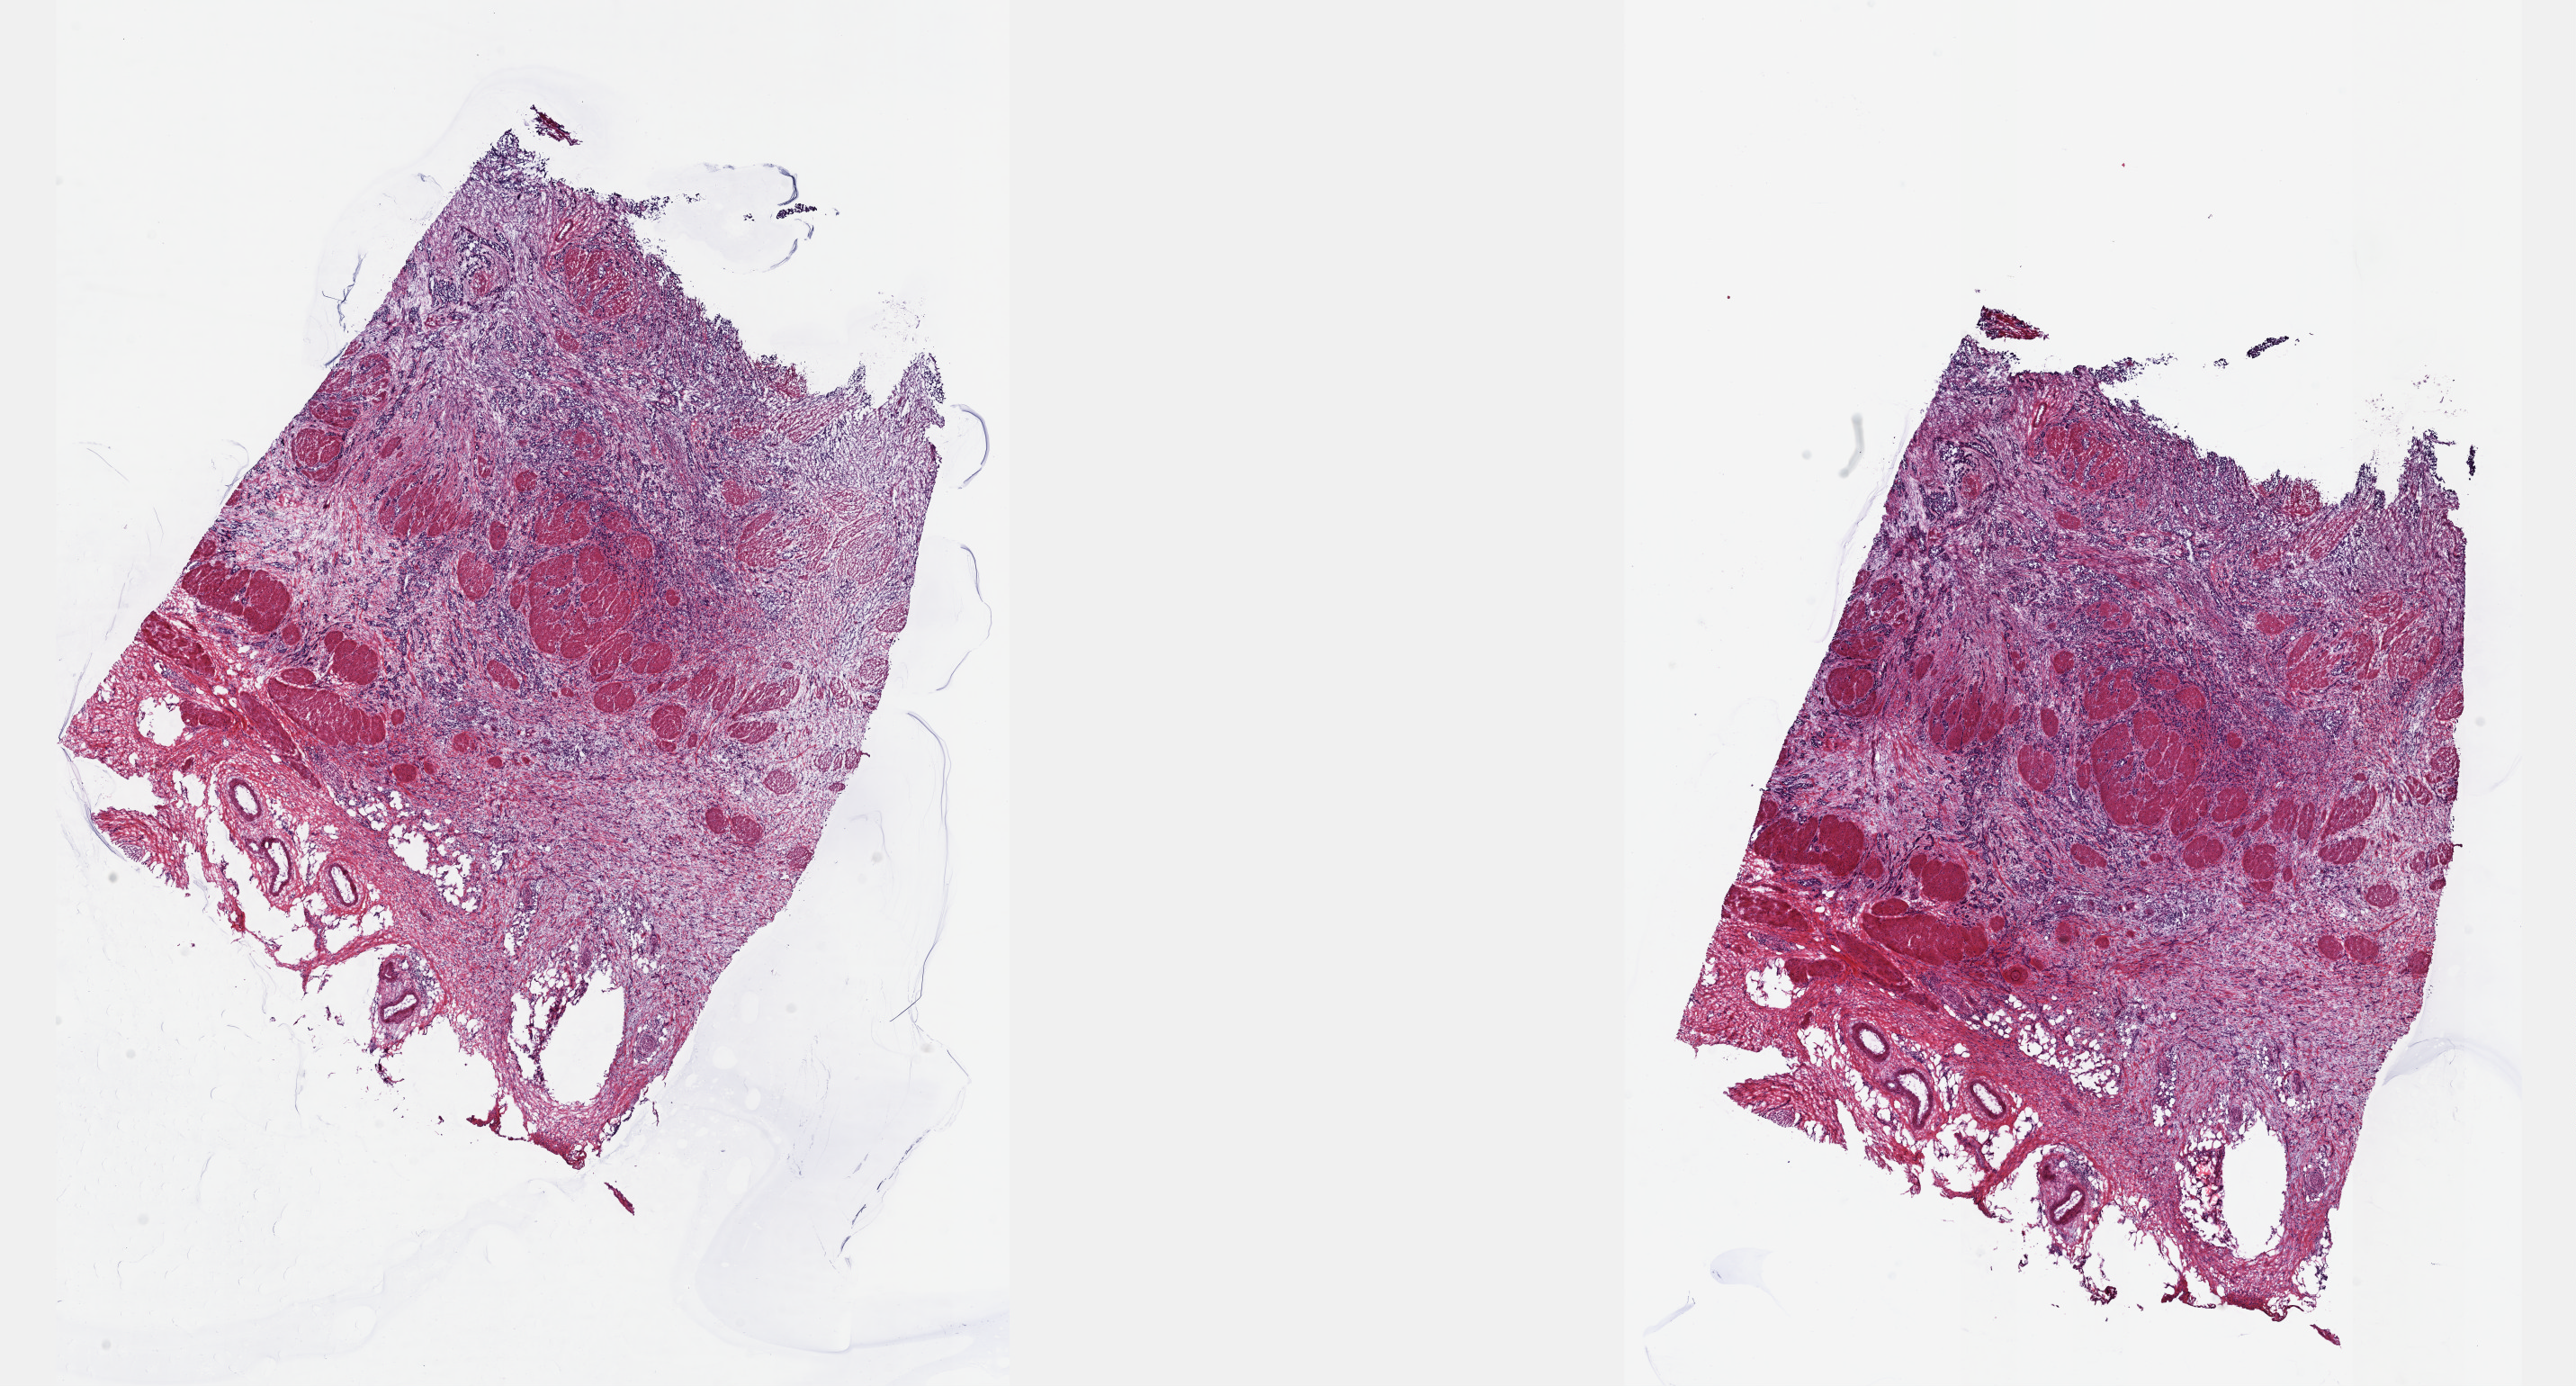
H&E whole-slide image, whole scanned area (about 23.1 x 12.4 mm) shown as a low-resolution overview, frozen section, primary tumour sample from the bladder. Male, age 59 years at initial diagnosis. Histologic grade: high grade. Pathologist review of this section (percent, as recorded): tumour cells 70%, tumour nuclei 70%, normal cells 0%, stromal cells 30%, necrosis 0%. Inflammatory infiltration, as recorded: lymphocyte infiltration 2%, monocyte infiltration 1%, neutrophil infiltration 6%.
TNM: T3b N0 MX. AJCC pathologic stage: III (6th edition). Pathologic diagnosis: Transitional cell carcinoma.